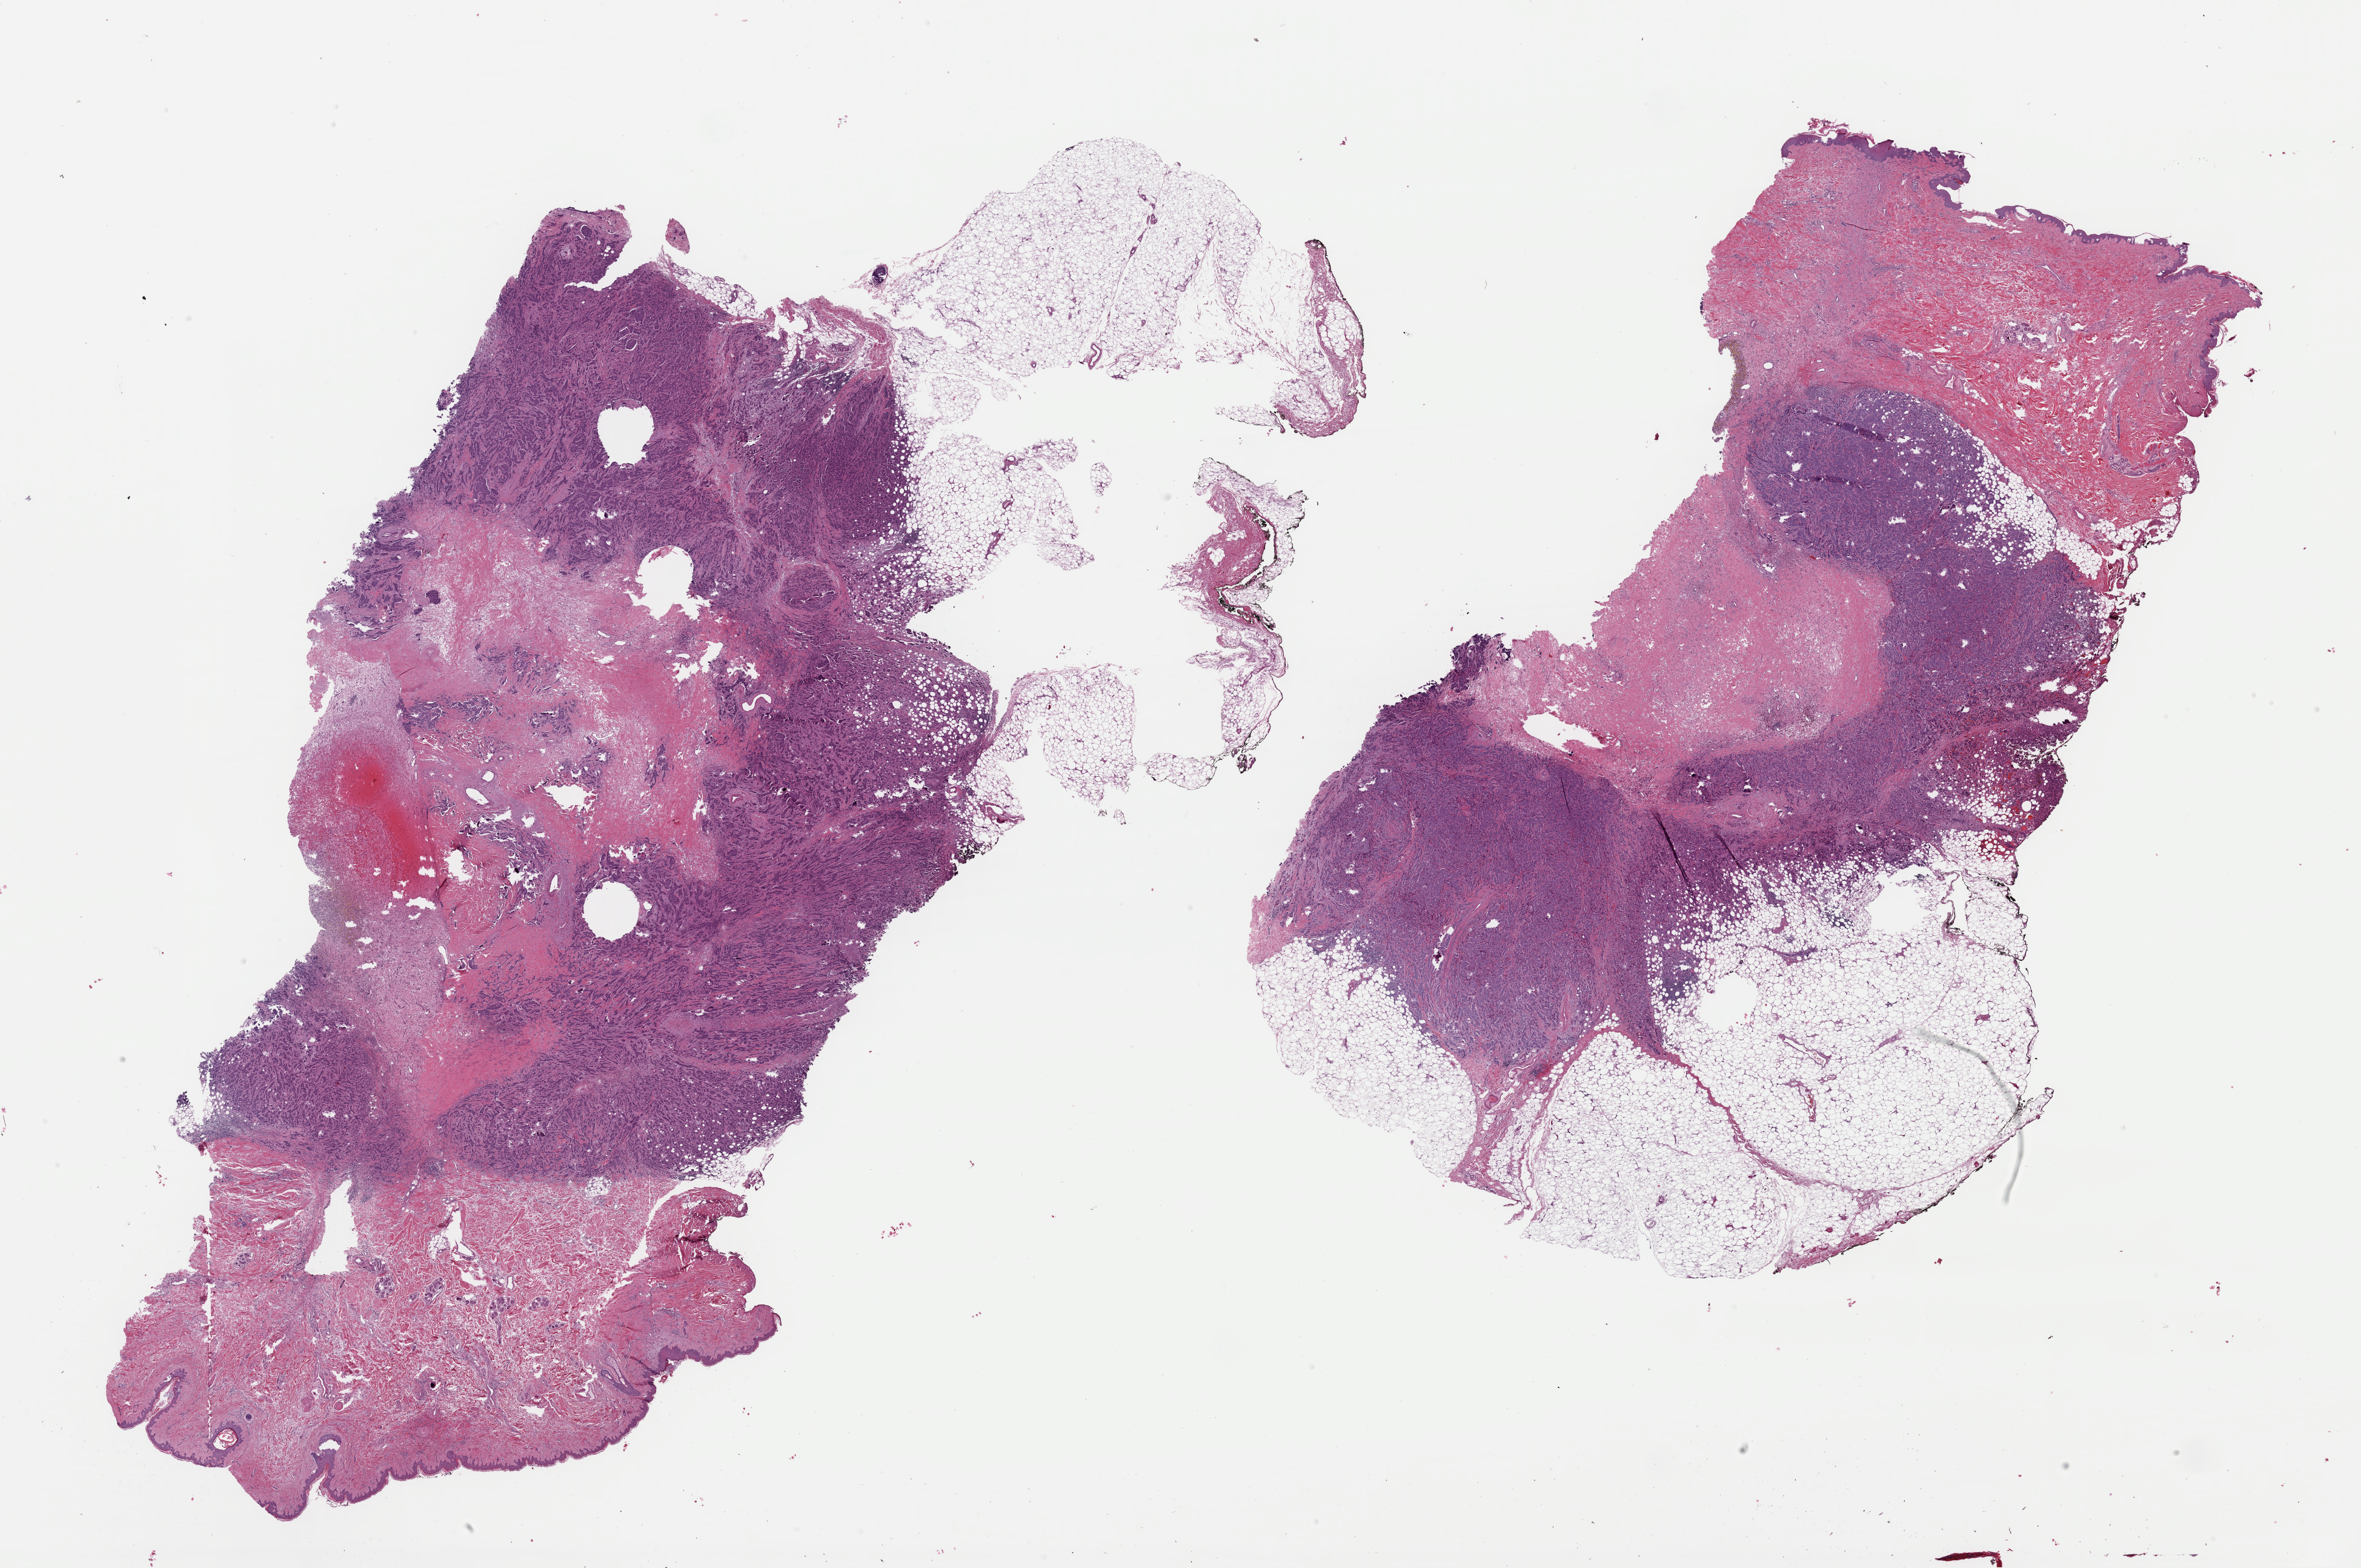
Whole-slide histology image, H&E-stained, whole scanned area (about 30.8 x 20.4 mm, slide scanned at 40x) shown as a low-resolution overview; formalin-fixed paraffin-embedded (FFPE) diagnostic section; sample: primary tumour, breast. Patient: female, age at initial diagnosis 68 years.
Histologic diagnosis: Infiltrating duct carcinoma, NOS. AJCC pathologic stage: IIB. Laterality: left.